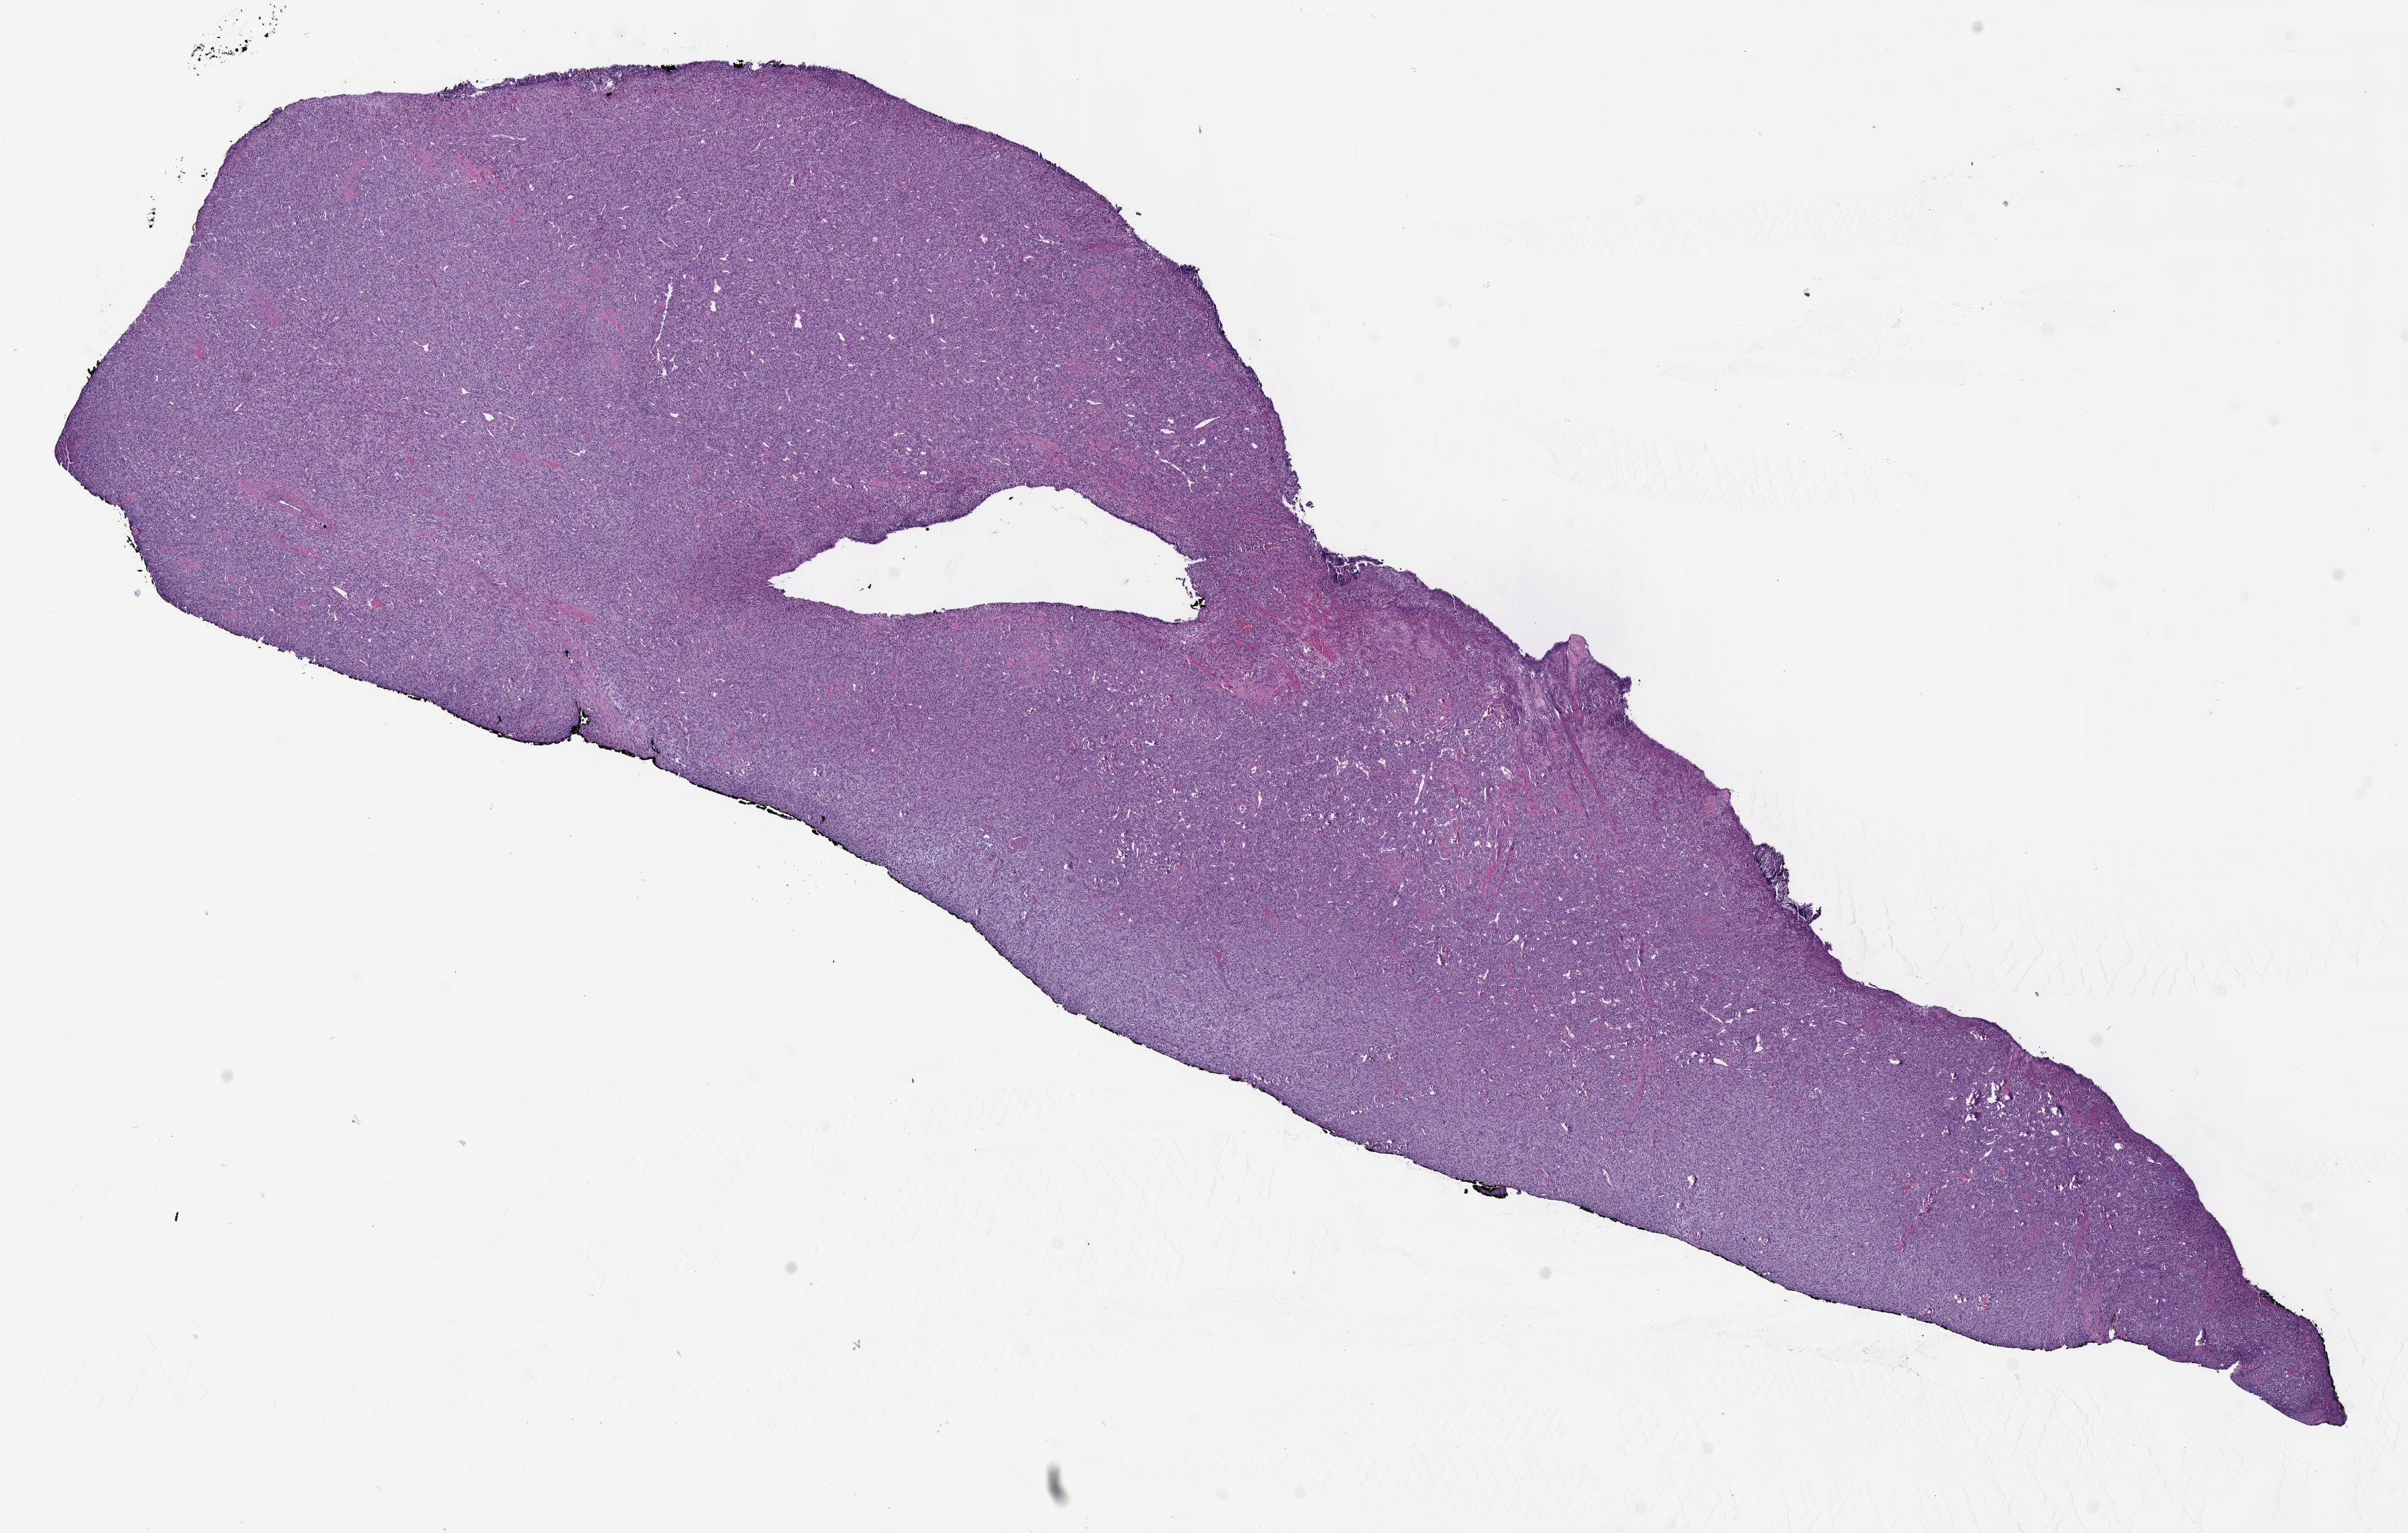
H&E whole-slide image, a low-resolution overview of the entire scanned area, about 14.2 x 9.0 mm (acquisition: 40x scan), formalin-fixed paraffin-embedded (FFPE) diagnostic section, primary tumour sample from the stomach. Patient: male, age at initial diagnosis 53 years.
Histologic diagnosis: Dedifferentiated liposarcoma.